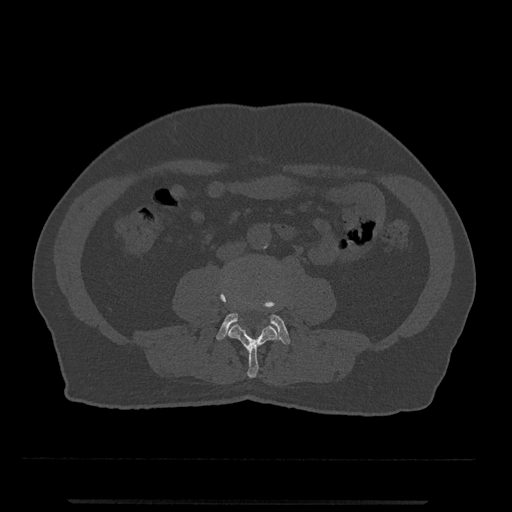
CT including the spine, one axial slice. Position 172 of 797 along the scan axis. Reconstruction kernel Br40s/3. Bone window (W 1800 / L 400 HU). 0.5 mm slice thickness. 512 × 512 image matrix, field of view 419 × 419 mm. Male patient, age 63 years. Case-level facts recorded for this patient, not image findings: primary cancer: prostate.
Annotated regions visible in this slice (semi-automatically segmented with operator editing):
- L3 vertebra: bounding box <220,292,278,378> (left, top, right, bottom; pixels)
- L4 vertebra: <217,301,290,345>